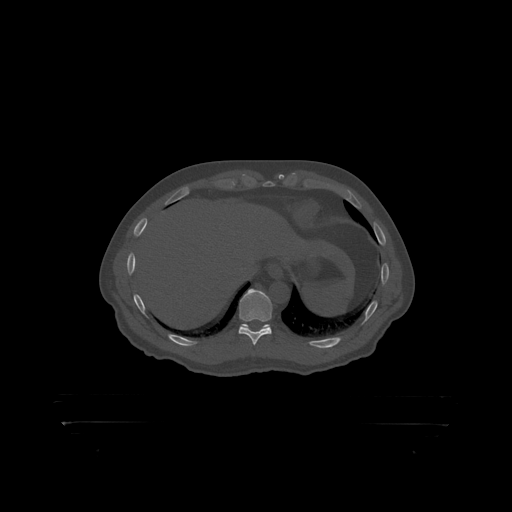
CT including the spine, one axial slice; reconstruction kernel STANDARD; 120 kVp; bone window (W 1800 / L 400 HU); 512 × 512 image matrix. Male patient, age 46 years. From the clinical record (not read from this slice): primary cancer: skin.
Structures marked on this image (semi-automatic segmentation, software-assisted and operator-edited):
- T10 vertebra: bounding box (x1, y1, x2, y2) in pixels: (240, 289, 273, 319)